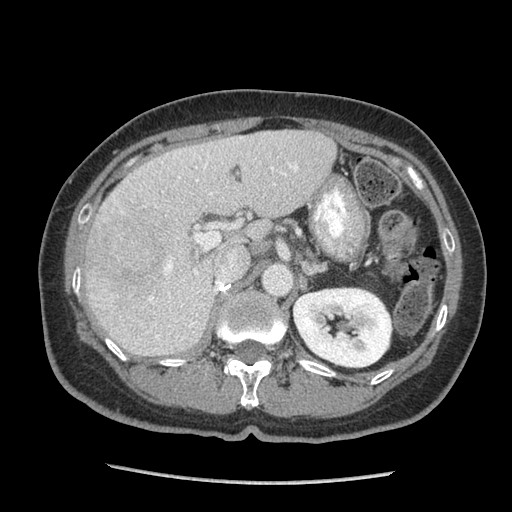
Contrast-enhanced abdominal CT (liver protocol), one axial slice. Position 49 of 105 along the scan axis. 140 kVp. Soft-tissue window (W 400 / L 40 HU). 2.5 mm slice thickness. 512 × 512 image matrix. Case-level facts recorded for this patient, not image findings: diagnosis: hepatocellular carcinoma (patient treated with transarterial chemoembolisation; whether this scan precedes or follows treatment is not stated here); TNM stage (as recorded): Stage-I.
Outlined on this slice (semi-automatic segmentation, software-assisted and operator-edited):
- liver parenchyma outside the tumour (the mass and vessels are separate outlines, so this box may not span the whole liver): box from (x=86, y=130) to (x=336, y=356) px
- mass: (x=87, y=207)–(x=173, y=288)
- liver vessels: (x=149, y=152)–(x=298, y=340)